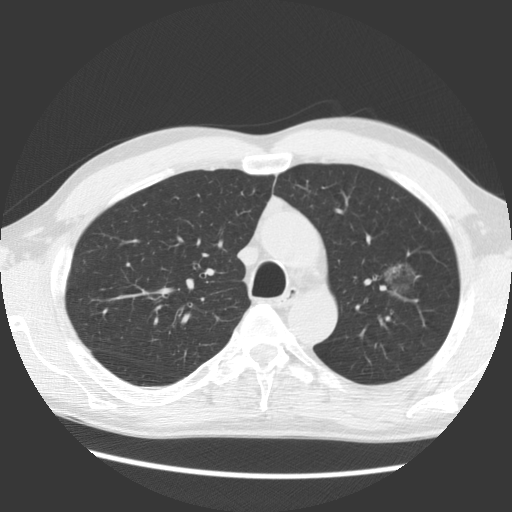
Chest CT (low-dose screening protocol), one axial image. Baseline annual screen. Lung window (W 1500 / L -600 HU). Standard (soft-tissue) reconstruction kernel (STANDARD). 140 kVp. 512 × 512 image matrix, field of view 340 × 340 mm. Male participant, aged 61 years at enrolment.
- Expert reader's lesion annotation, bounding box <357,238,443,313> (left, top, right, bottom; pixels).
- Reader record for this screening exam (exam-level; its link to the box is not recorded): non-calcified nodule or mass ≥4 mm, left upper lobe, 17 × 14 mm, soft tissue attenuation.
- Official screen result: positive, change unspecified: nodule(s) >= 4 mm or enlarging nodule(s), mass(es), or other non-specific abnormalities suspicious for lung cancer.
- Later outcome: lung cancer diagnosed 1061 days after this screen (after the third annual screen) — bronchiolo-alveolar adenocarcinoma, NOS, left upper lobe, well differentiated (G1), stage IB (AJCC 6th edition), 44 mm at pathology.